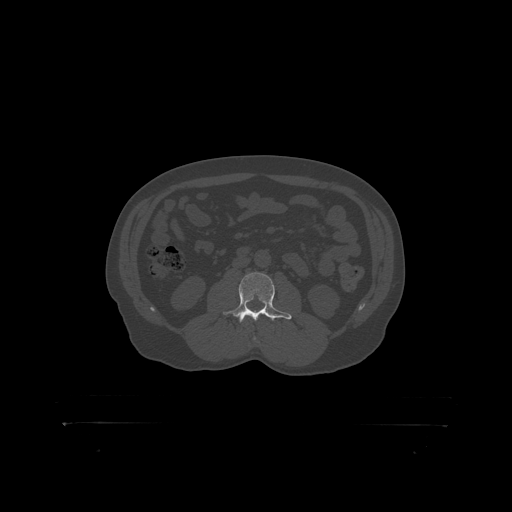
CT including the spine, one axial slice; position 269 of 399 along the scan axis; reconstruction kernel STANDARD; 120 kVp; bone window (W 1800 / L 400 HU); 512 × 512 image matrix, field of view 650 × 650 mm. Patient: male, 46 years. From the clinical record (not read from this slice): primary cancer: skin.
Outlined on this slice (semi-automatically segmented with operator editing):
- L3 vertebra: bounding box [x1, y1, x2, y2] px = [229, 273, 282, 319]